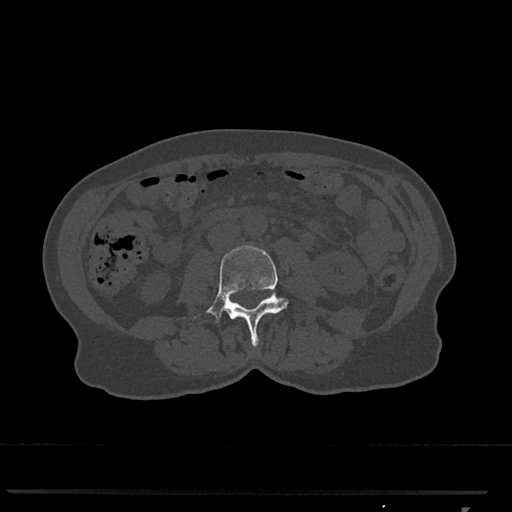
CT including the spine, one axial slice; slice 271 of 793 in the series (ordered by position); bone window (W 1800 / L 400 HU); 512 × 512 image matrix, field of view 380 × 380 mm. Patient: female, 62 years. Case-level facts recorded for this patient, not image findings: primary cancer: renal.
Outlined on this slice (semi-automatically segmented with operator editing):
- L3 vertebra: bounding box [x1, y1, x2, y2] px = [194, 245, 289, 347]